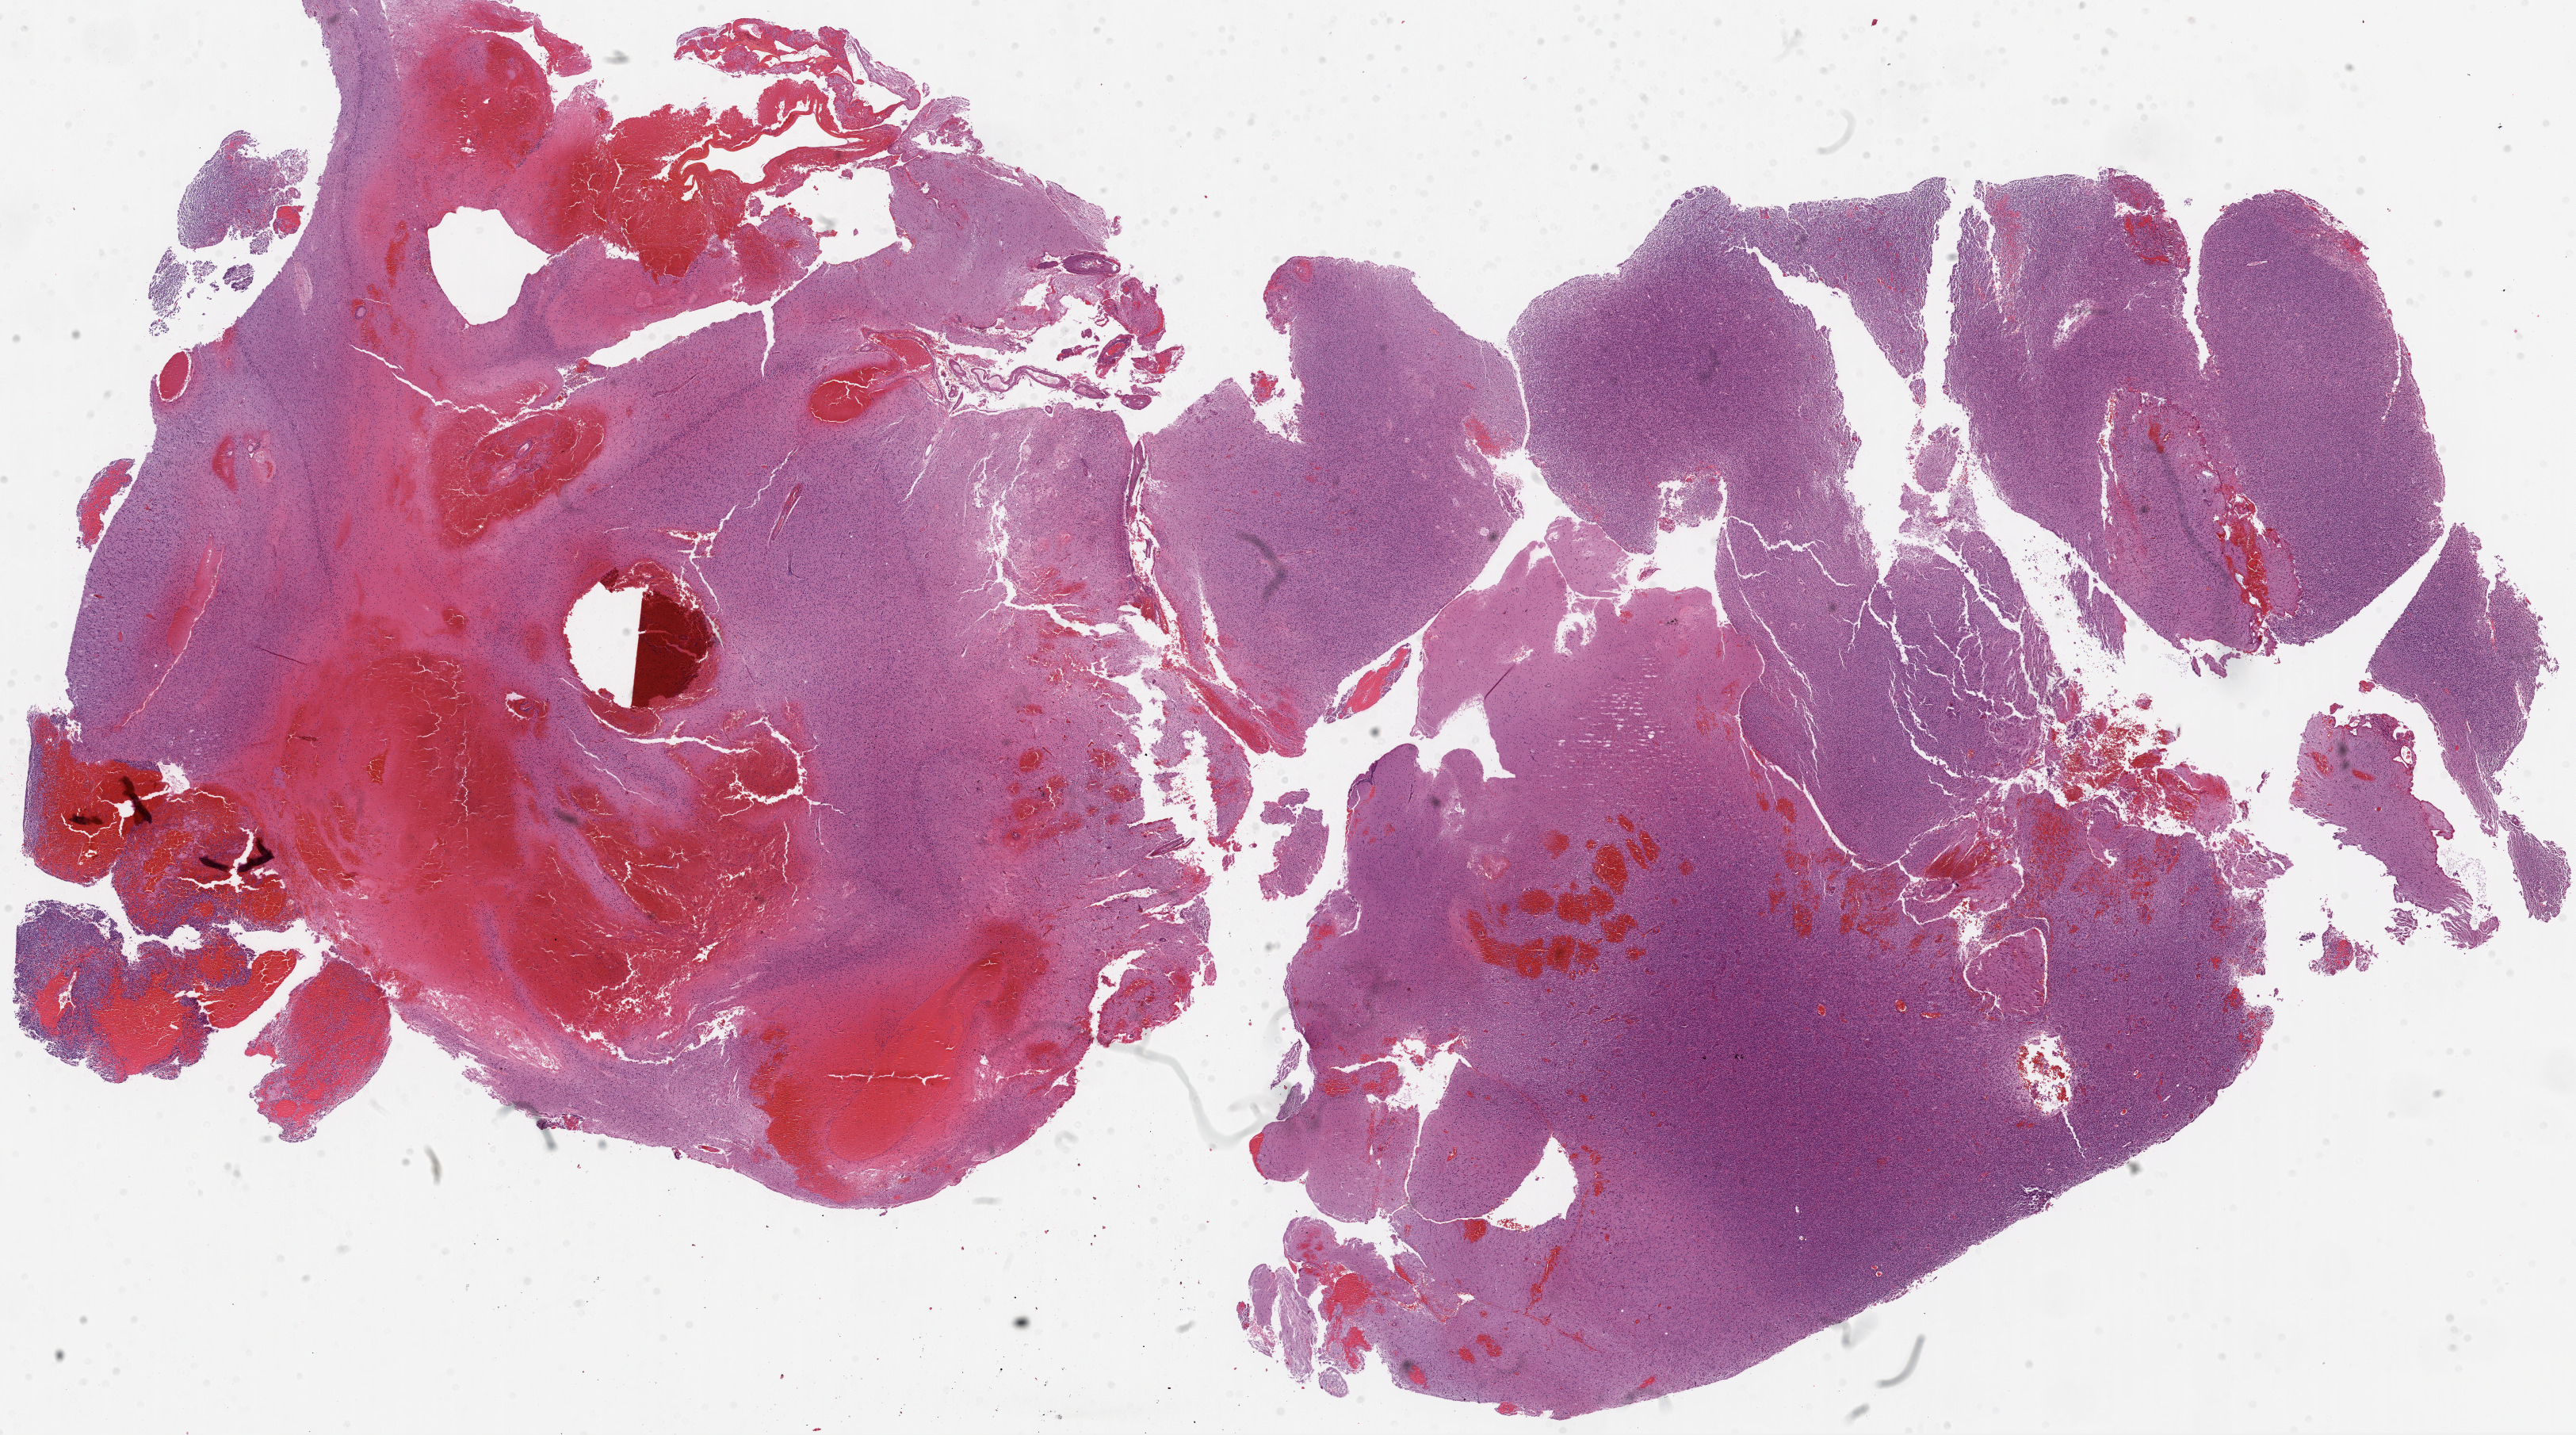
H&E whole-slide image, low-resolution overview of the scanned area, about 26.1 x 14.5 mm, formalin-fixed paraffin-embedded (FFPE) diagnostic section, sample: primary tumour, brain. Female patient; age at initial diagnosis 43 years.
• pathologic diagnosis: Glioblastoma